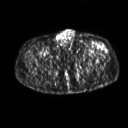
FDG PET of an extremity soft-tissue mass (from a PET/CT study), one axial slice. Position 260 of 267 along the scan axis. 3.27 mm slice thickness. 128 × 128 image matrix. Patient: male, 64 years. From the clinical record (not read from this slice): histological type: extraskeletal osteosarcoma; grade: high; site of the primary tumour: thigh.
Outlined on this slice (expert contour drawn on MRI and transferred to this co-registered scan by the dataset authors):
- gross tumour volume (mass): bounding box [x1, y1, x2, y2] px = [94, 43, 105, 48]